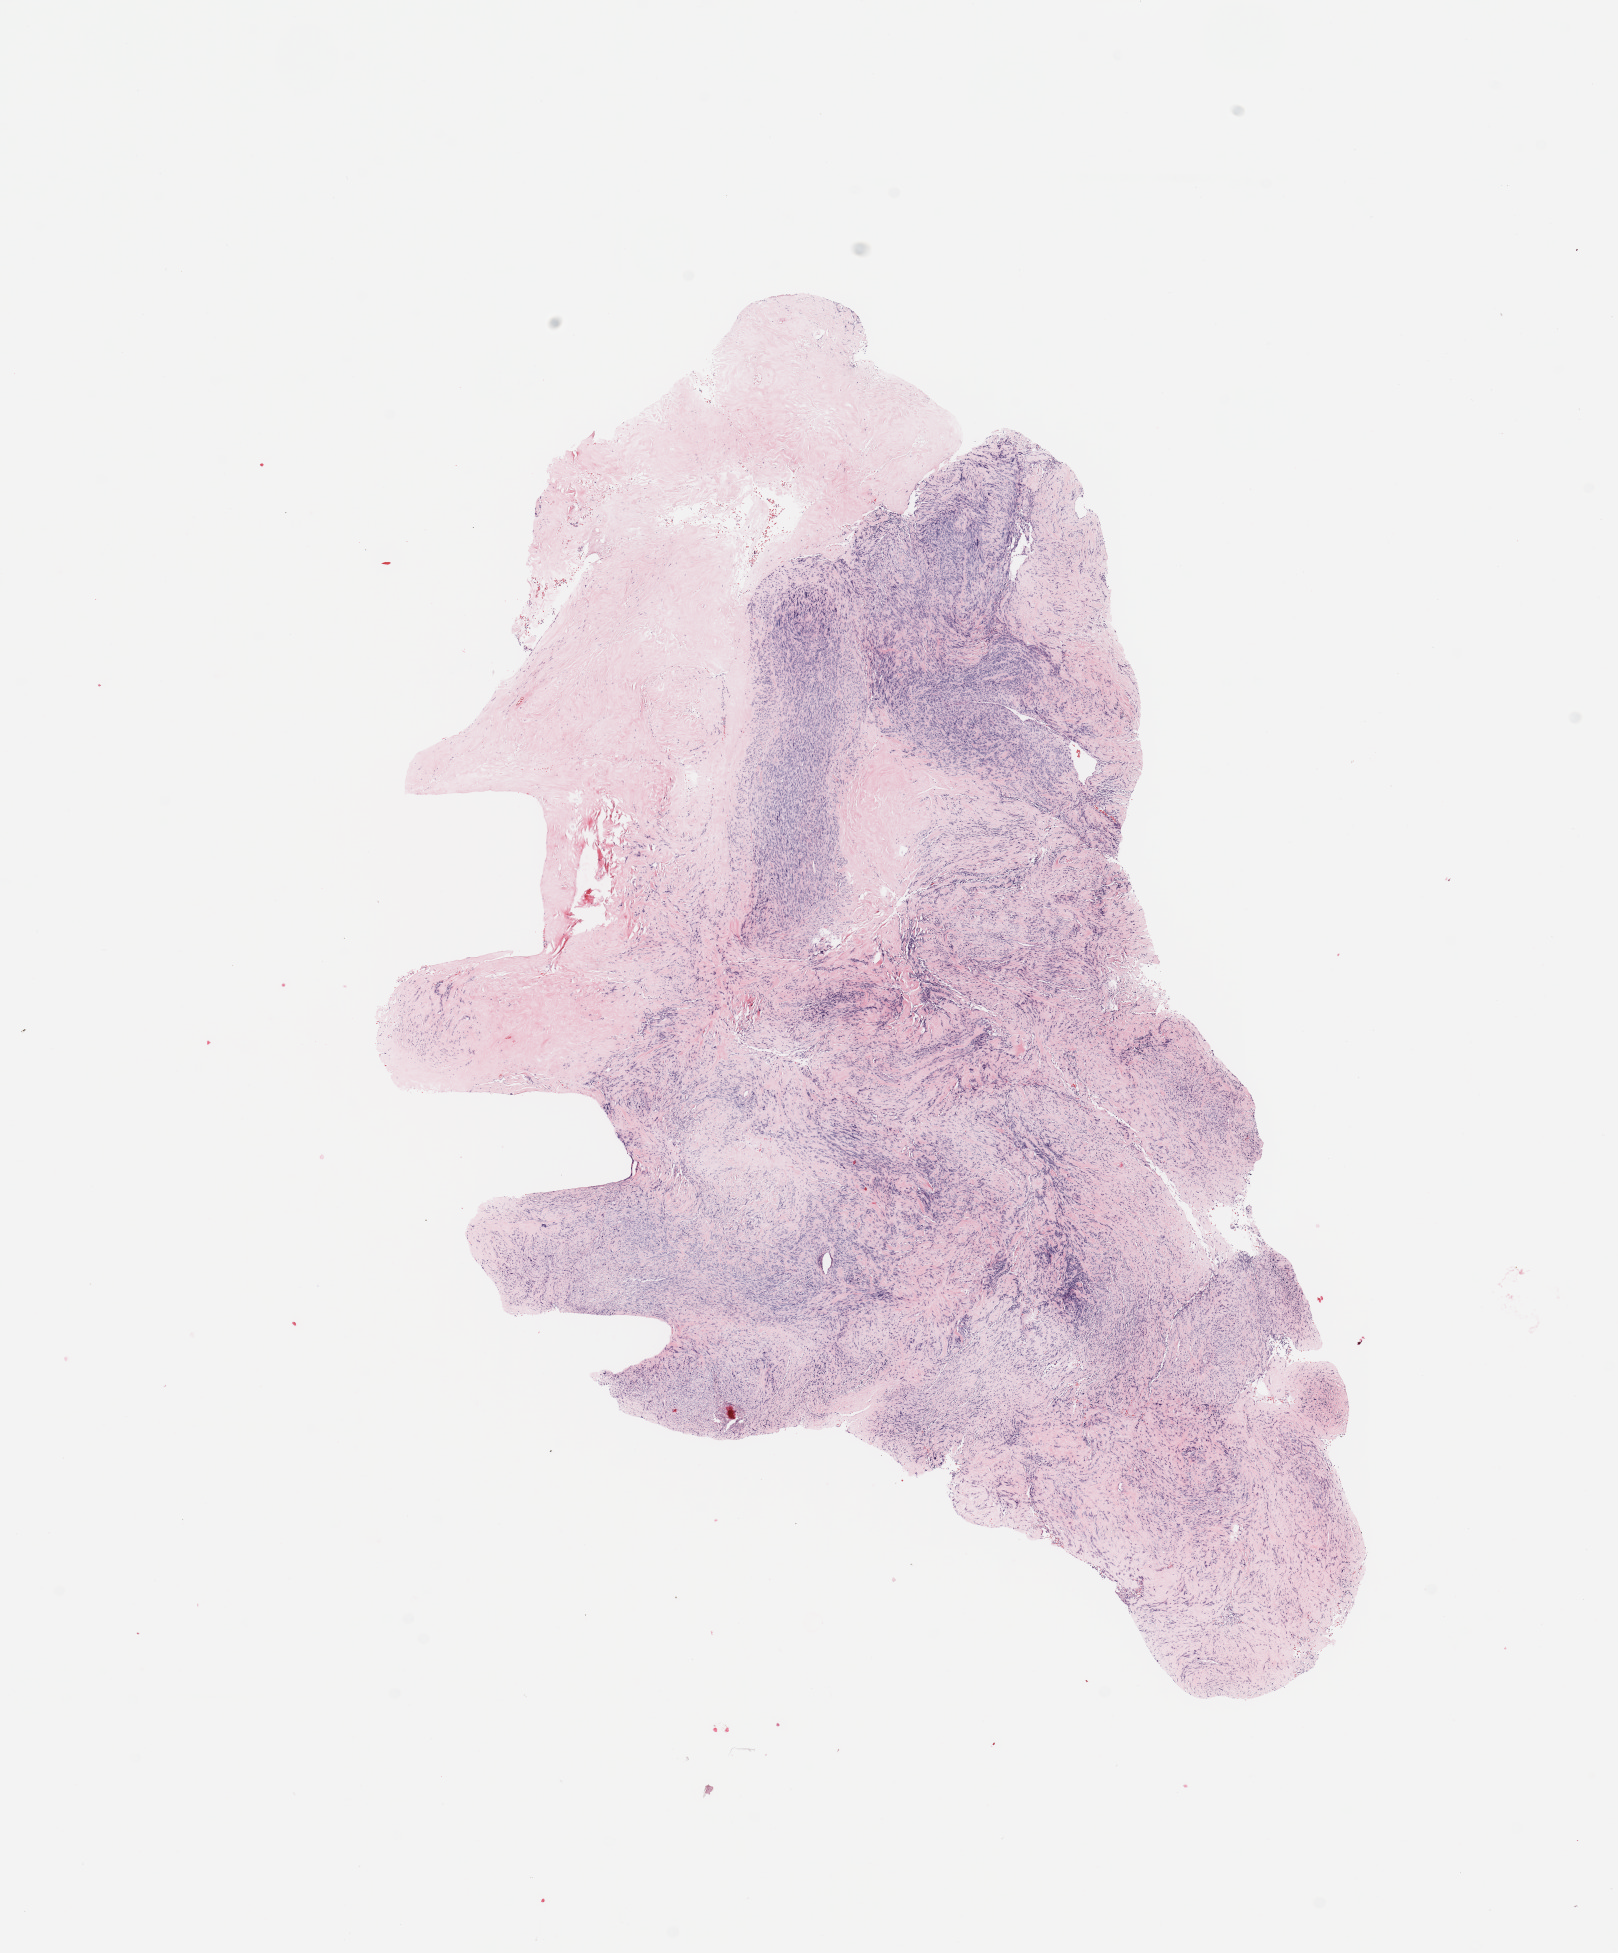
Hematoxylin and eosin (H&E) stained whole-slide image — a low-resolution overview of the entire scanned area, about 12.8 x 15.4 mm. 66-year-old male patient.
Primary tumour site (as recorded): pelvic. Patient diagnosis (cohort enrolment): sarcoma (site not recorded at cohort level).